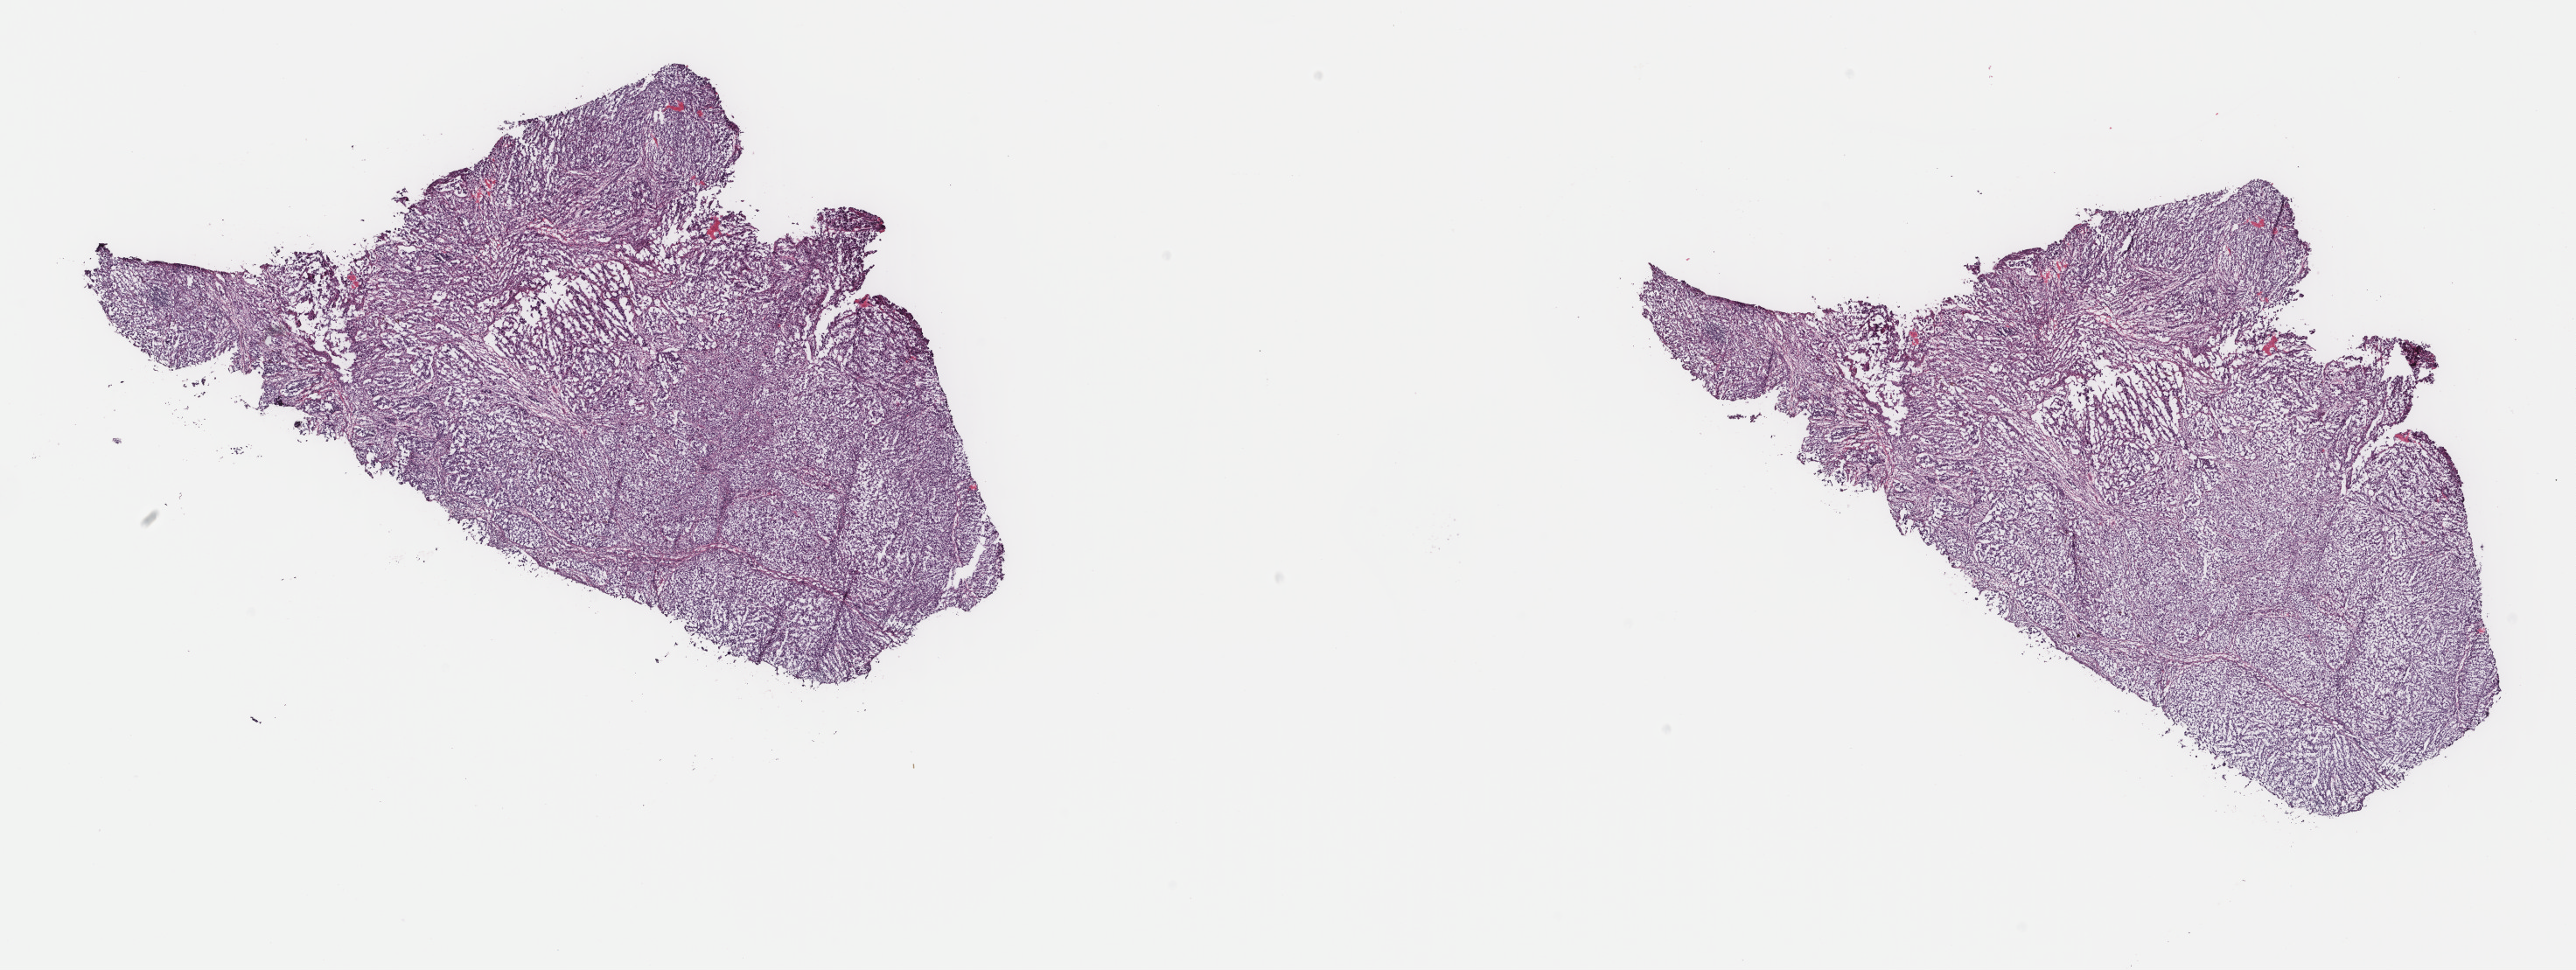
Digitized H&E-stained tissue section (whole slide) — whole scanned area (about 23.4 x 8.8 mm, from a 40x scan) shown as a low-resolution overview. Frozen section from the top of the tissue portion. Metastatic tumour sample, sampled site not recorded. Female, age 61 years at initial diagnosis. Pathologist review of this section (percent, as recorded): tumour cells 85%, tumour nuclei 85%.
This section: metastatic tumour tissue. Patient diagnosis: Malignant melanoma, NOS.